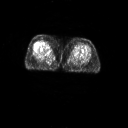
FDG PET of an extremity soft-tissue mass (from a PET/CT study), one axial slice; slice 13 of 267 in the series (ordered by position); 3.27 mm slice thickness; 128 × 128 image matrix. Patient: female, 56 years. Case-level facts recorded for this patient, not image findings: histological type: malignant solitary fibrous tumor; grade: intermediate; site of the primary tumour: right thigh.
Outlined on this slice (expert contour drawn on MRI and transferred to this co-registered scan by the dataset authors):
- gross tumour volume including surrounding oedema: bounding box [x1, y1, x2, y2] px = [41, 41, 51, 48]